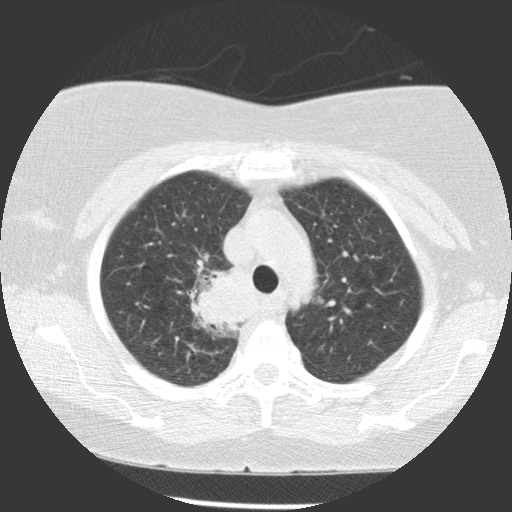
Low-dose screening chest CT, axial slice, first (baseline) screen, lung window (W 1500 / L -600 HU), standard (soft-tissue) reconstruction kernel (STANDARD), 140 kVp, slice 89 of 116 in the series, 512 × 512 image matrix, field of view 320 × 320 mm. Female, age 63 years at enrolment. Former smoker at enrolment.
Expert reader's lesion annotation, bounding box <197,266,256,327> (left, top, right, bottom; pixels). The exam's reader record, not a measurement of the box and not confirmed to be the same lesion: non-calcified nodule or mass ≥4 mm, right upper lobe, 39 × 36 mm, spiculated (stellate) margins, soft tissue attenuation. Participant outcome: lung cancer diagnosed 72 days after this screen — non-small cell carcinoma, right upper lobe, carina, right main stem bronchus, poorly differentiated (G3), stage IIIA (AJCC 6th edition), 66 mm at pathology.